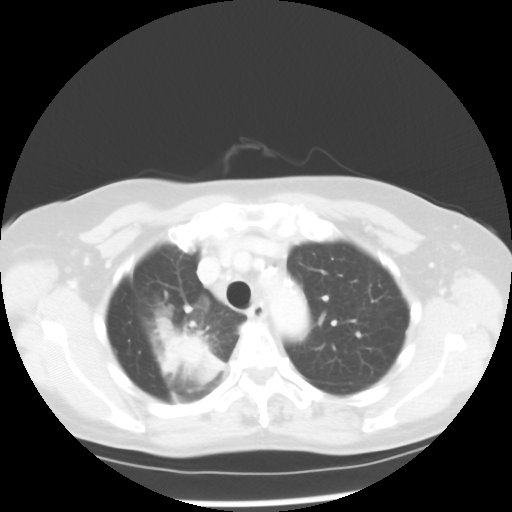
Chest CT, one axial slice; reconstruction kernel STANDARD; 100 kVp; lung window (W 1500 / L -600 HU); 512 × 512 image matrix. Female patient, age 60 years. From the clinical record (not read from this slice): clinical TNM (as recorded): T2 N1 M1a.
Annotated regions visible in this slice (bounding box drawn by a radiologist):
- lung tumour (recorded histology: adenocarcinoma): bounding box (x1, y1, x2, y2) in pixels: (146, 305, 231, 391)